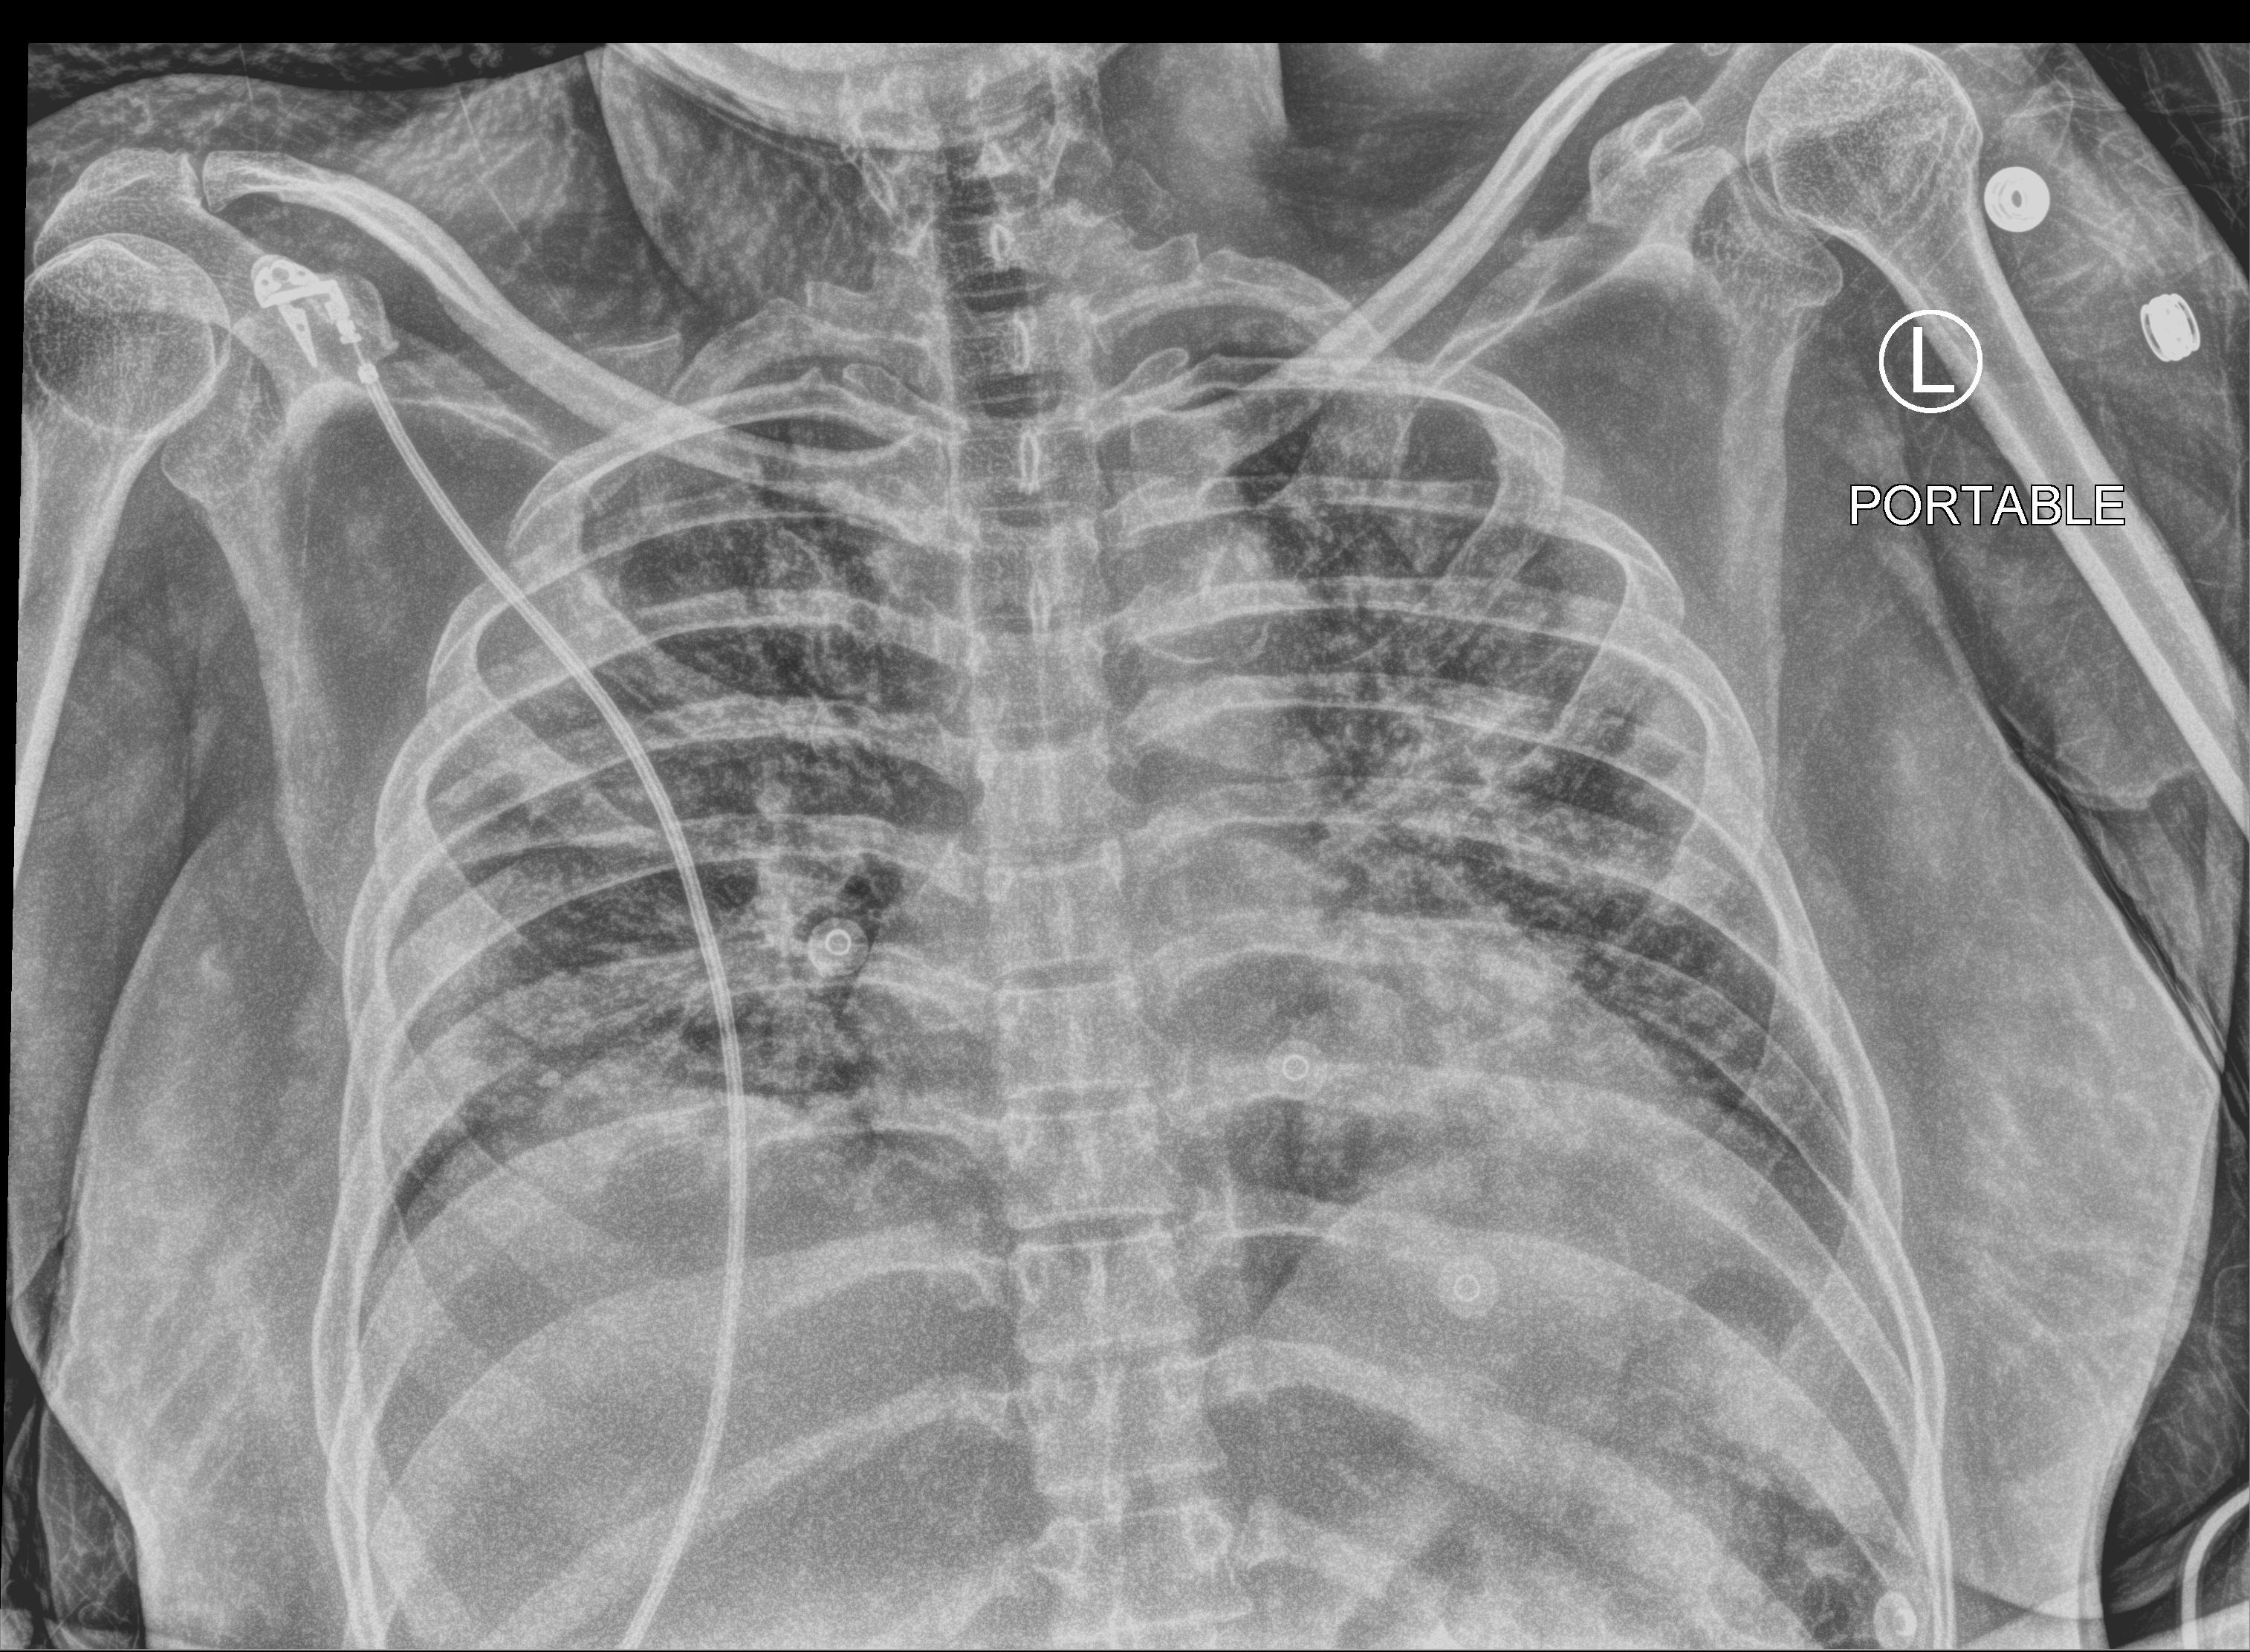
Chest X-ray (portable); anteroposterior (AP) projection. Adult patient hospitalised with COVID-19, age 18–59 years.
Admission-level facts for this patient (not findings on this image; timing relative to this image not recorded):
- mechanically ventilated during this hospital stay: yes